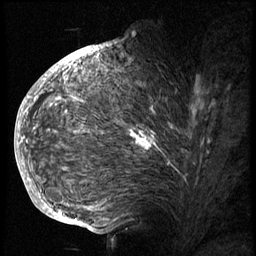
Breast MRI (dynamic contrast-enhanced), one sagittal slice; 3 images stored at this slice position (order not interpretable as contrast timing); 1.5 T; TE 4.2 ms, TR 8.9 ms; 2.5 mm slice thickness; 256 × 256 image matrix, field of view 200 × 200 mm. Female patient, age 57 years. From the clinical record (not read from this slice): setting: breast cancer imaged before/during neoadjuvant chemotherapy; receptor status: HER2-positive.
Outlined on this slice (semi-automatic segmentation, software-assisted and operator-edited):
- analysis volume of interest (the breast-tissue region the enhancement analysis was run in; not a lesion): box from (x=40, y=62) to (x=242, y=175) px
- tumour enhancement mask (voxels above the 140 % enhancement threshold inside the analysis volume of interest): (x=48, y=68)–(x=198, y=150)